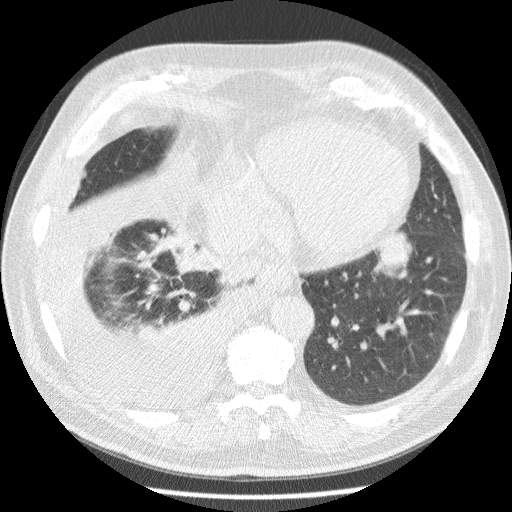
Low-dose screening chest CT, one axial slice. Slice 62 of 180 in the series (ordered by position). Reconstruction kernel STANDARD. 120 kVp. Lung window (W 1500 / L -600 HU). 2.5 mm slice thickness. 512 × 512 image matrix, field of view 355 × 355 mm.
Structures marked on this image (manually delineated by an expert):
- lesion 1 (tumor, lower lobe of left lung): bounding box [x1, y1, x2, y2] px = [379, 233, 412, 272]